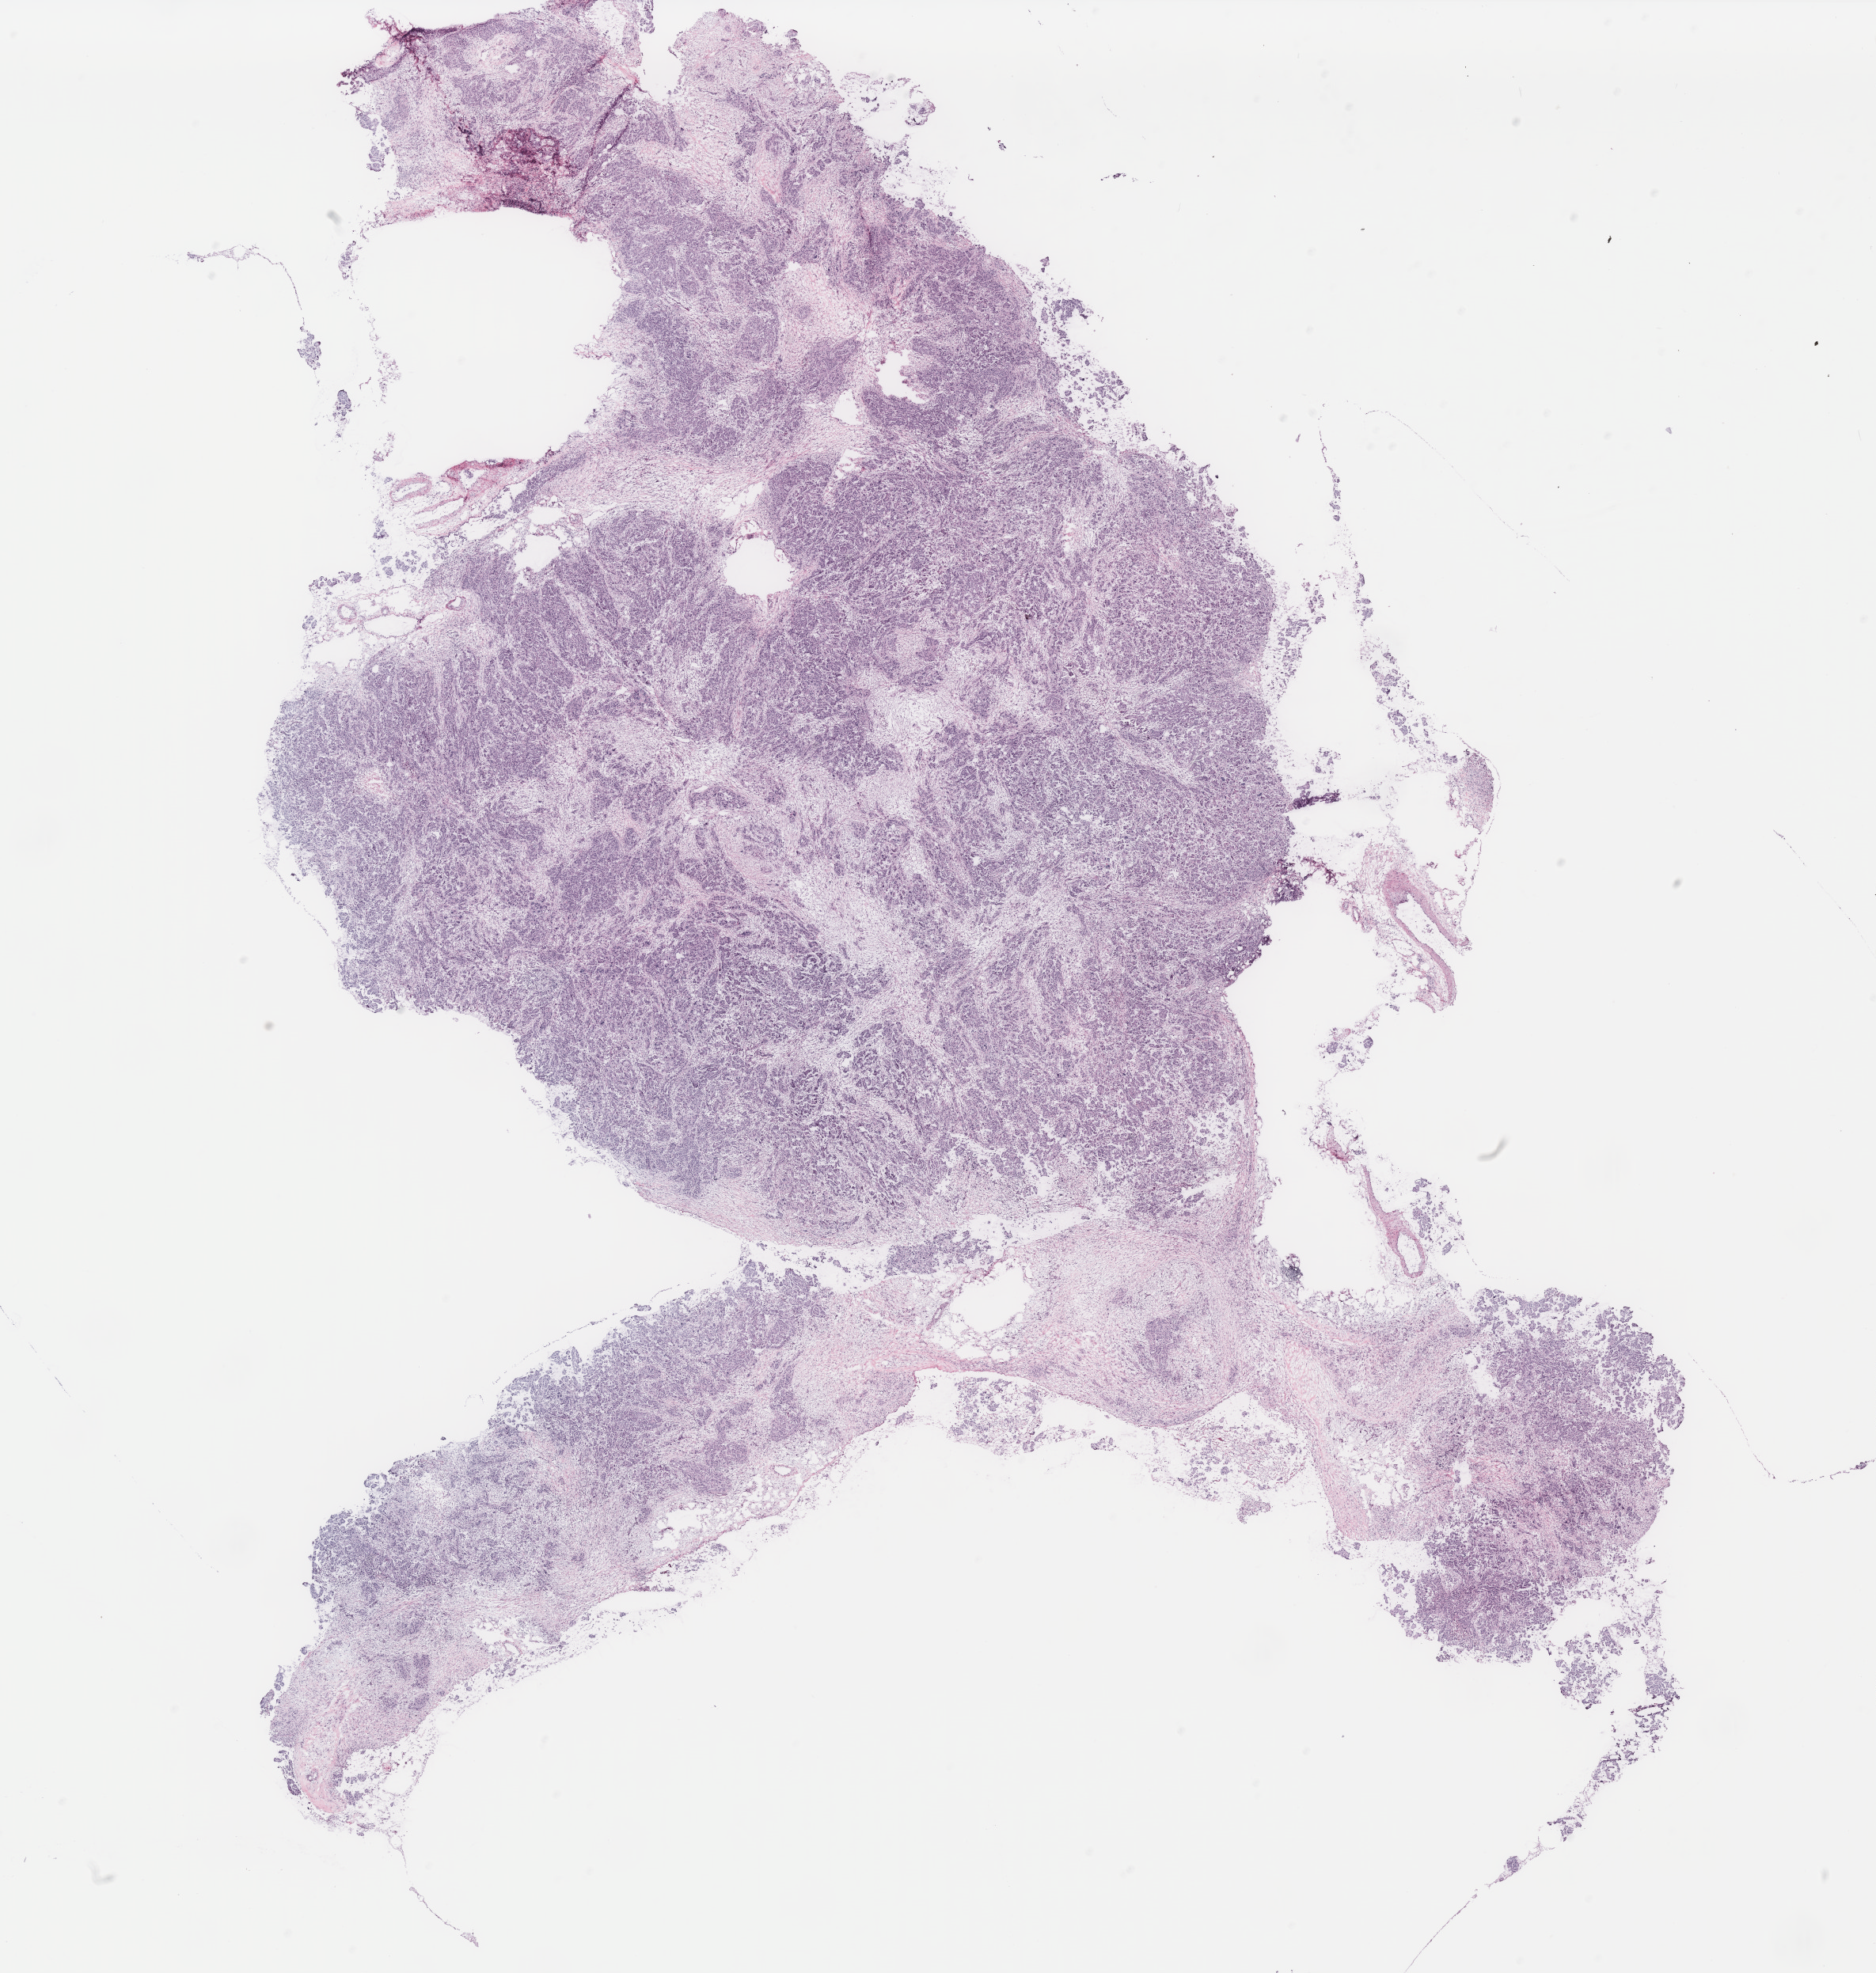
Hematoxylin and eosin (H&E) stained whole-slide image — shown as a low-resolution overview of the whole scanned area (about 19.0 x 20.0 mm, slide scanned at 40x). Tumour tissue sample, ovary. Patient: female, age 59 years.
Diagnosis: Serous adenocarcinoma, NOS. Primary tumour site (as recorded): ovary.